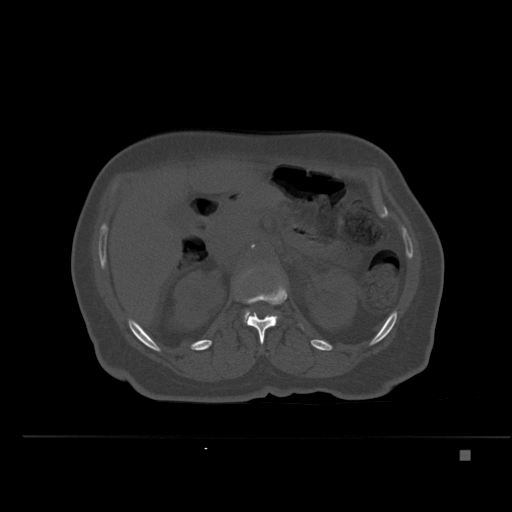
CT including the spine, one axial slice. Position 231 of 477 along the scan axis. Bone window (W 1800 / L 400 HU). 512 × 512 image matrix. Patient: female, 74 years. From the clinical record (not read from this slice): primary cancer: colon.
Annotated regions visible in this slice (semi-automatically segmented with operator editing):
- L1 vertebra: bounding box <238,283,304,344> (left, top, right, bottom; pixels)
- L2 vertebra: <244,310,250,322>